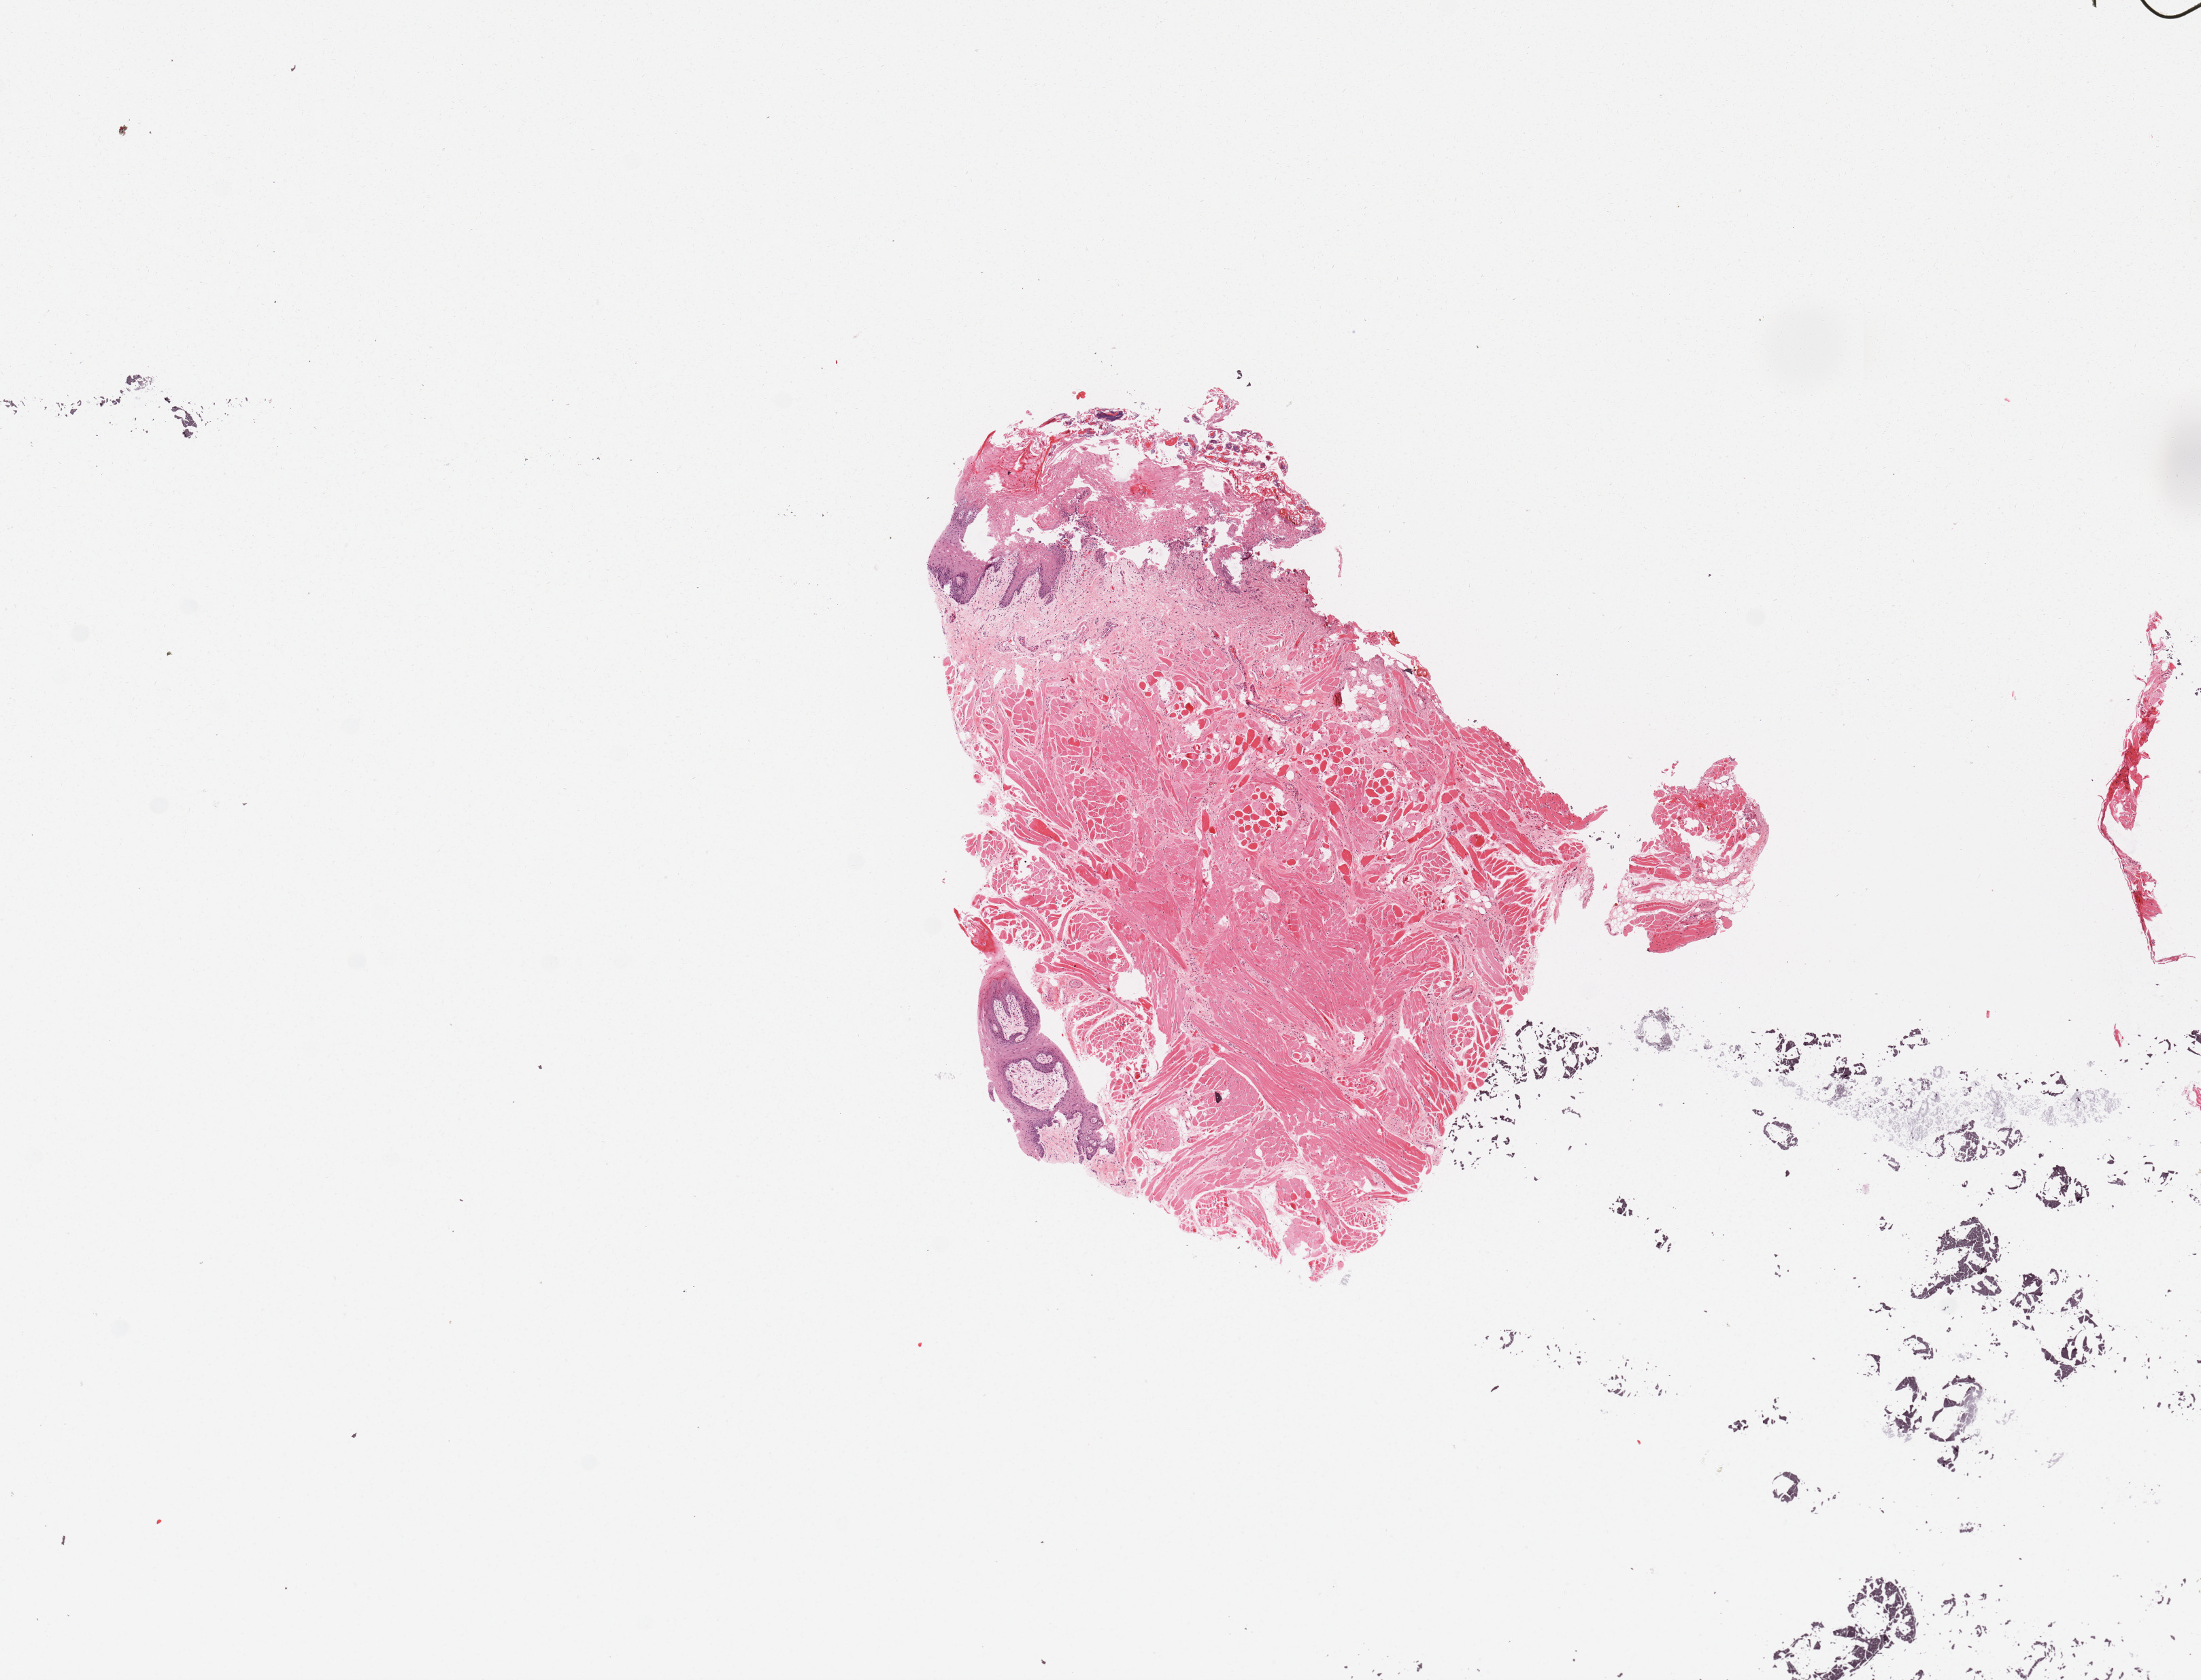
H&E-stained whole-slide image, low-resolution overview of the scanned area, about 12.8 x 9.8 mm. Head and neck, tissue type not recorded. Patient: male, age 40 years.
* patient diagnosis: Squamous cell carcinoma, NOS (tongue, NOS)